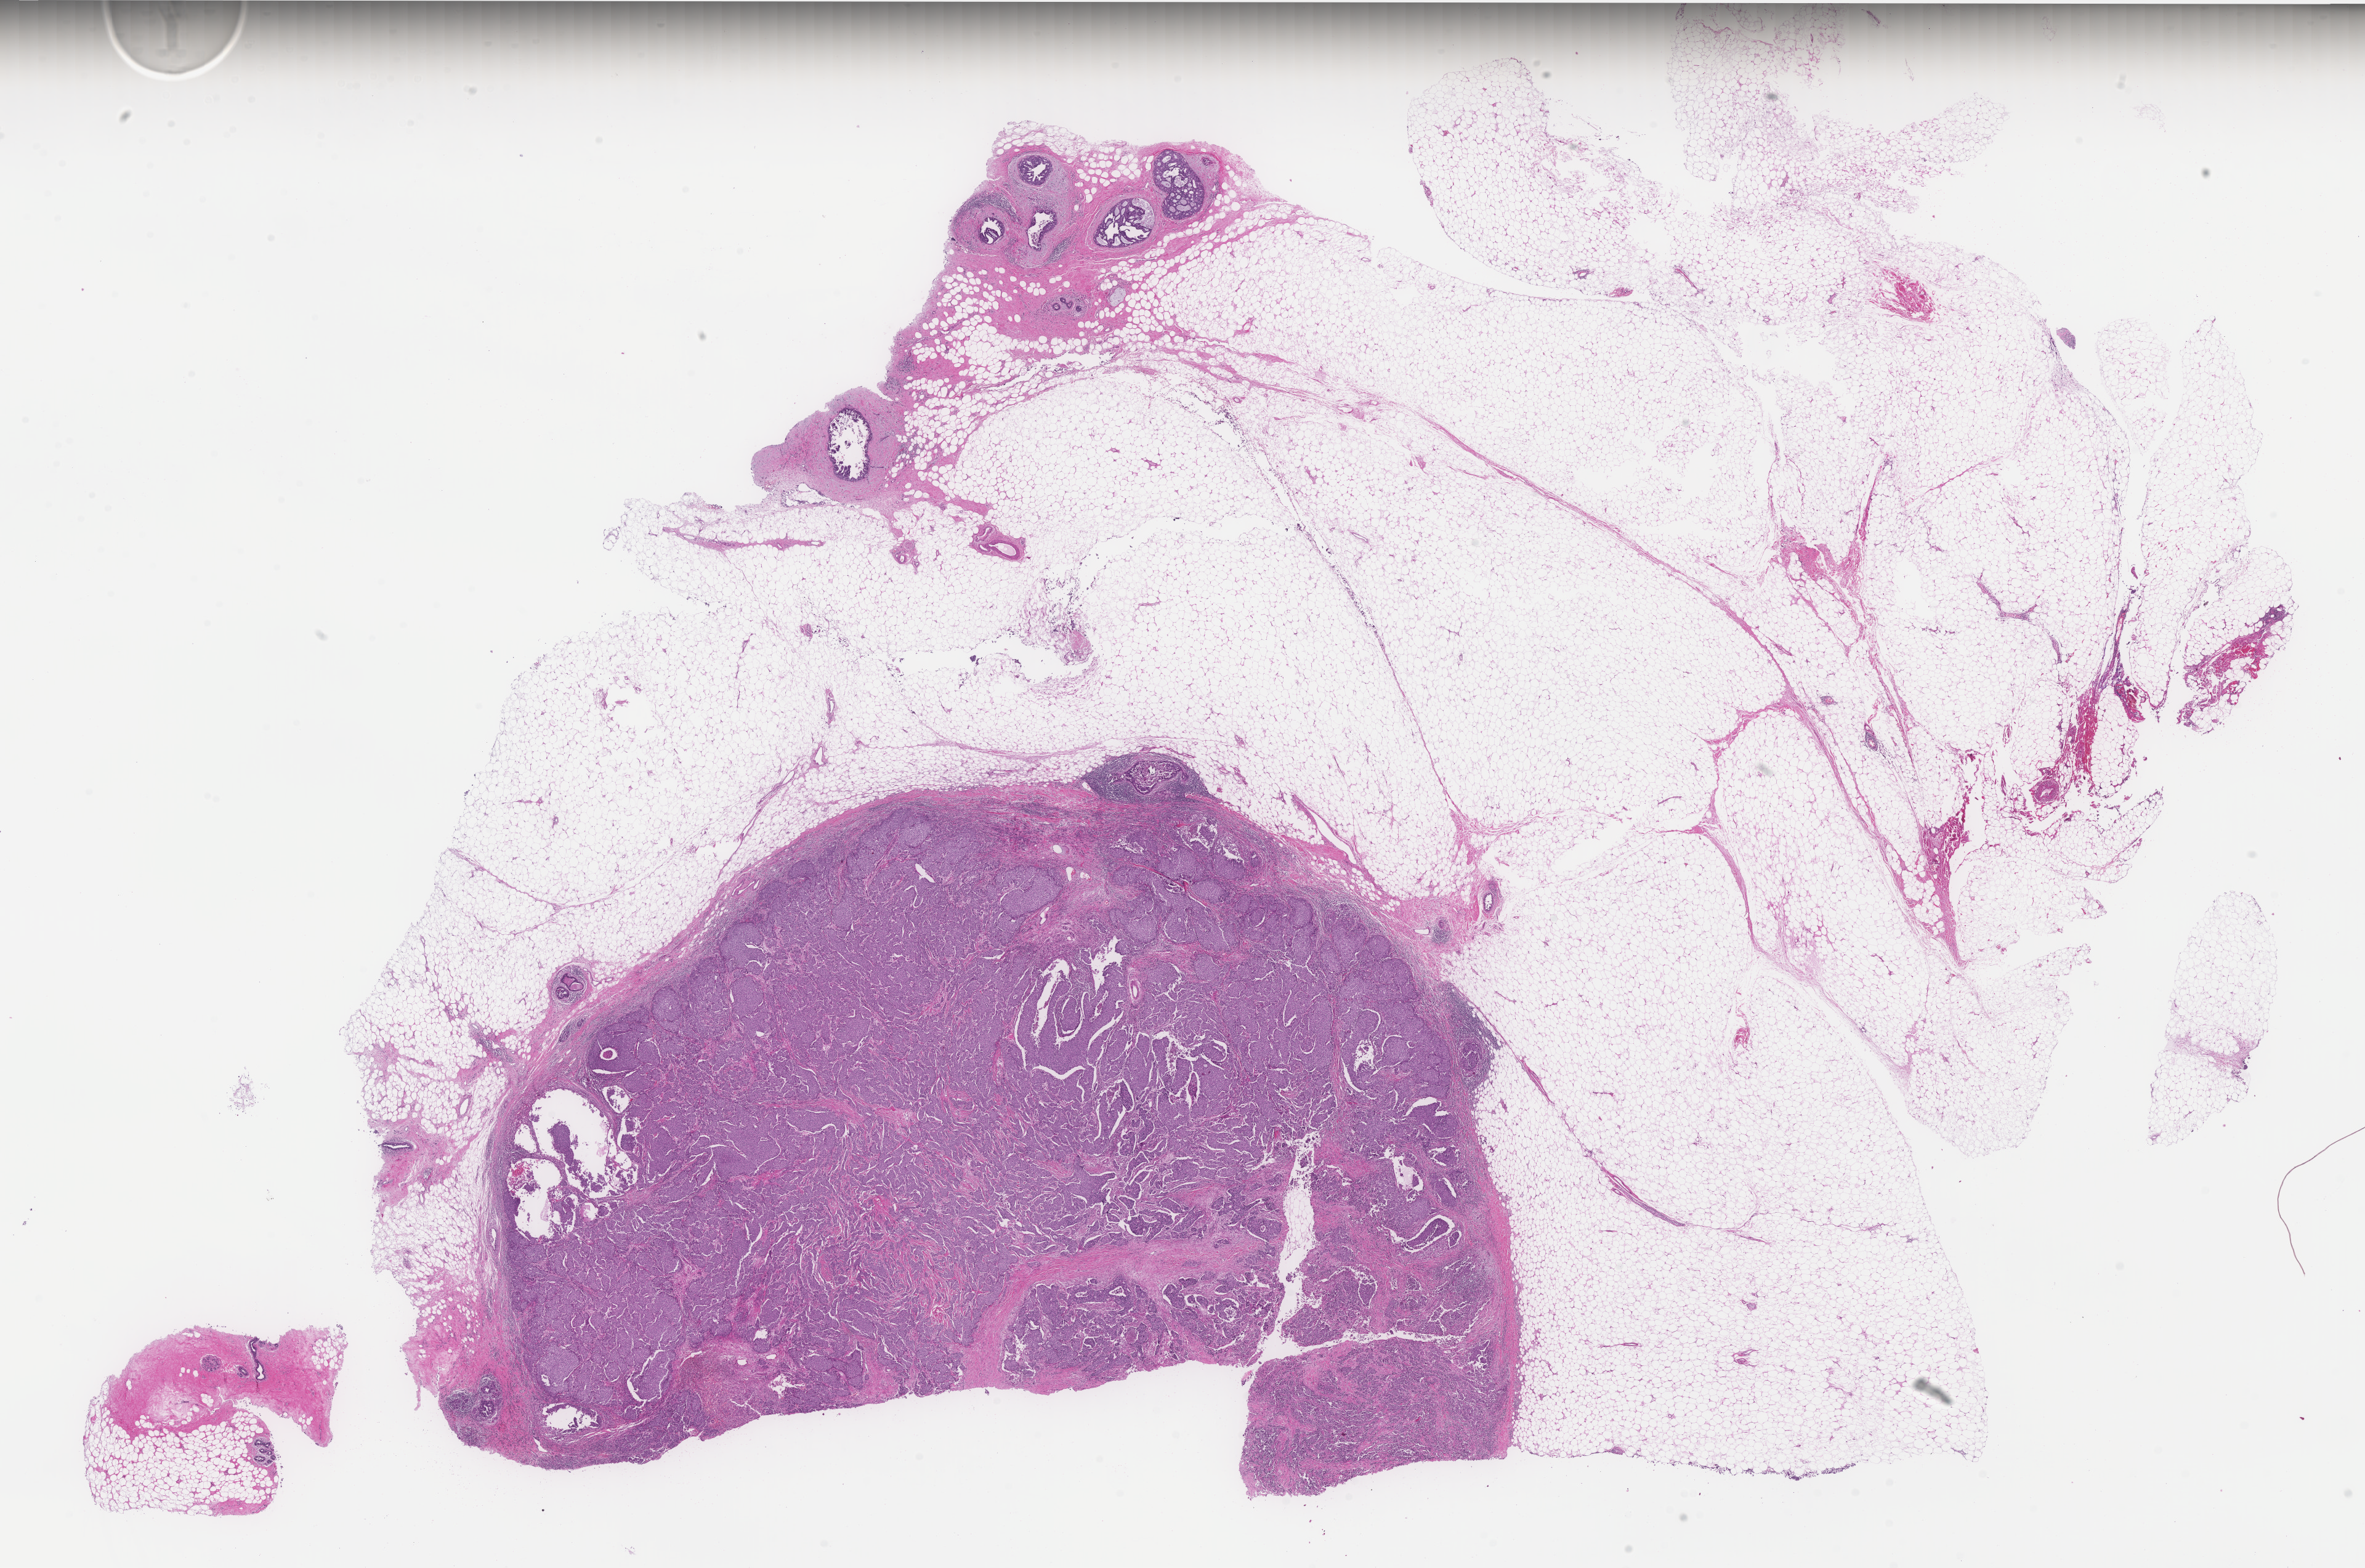
Whole-slide histology image, H&E-stained, whole scanned area (about 30.8 x 20.4 mm, from a 40x scan) shown as a low-resolution overview; FFPE section; primary tumour sample from the breast. Female patient; age at initial diagnosis 34 years.
Diagnosis: Infiltrating duct carcinoma, NOS. Laterality: left. AJCC pathologic stage: IIA (6th edition).